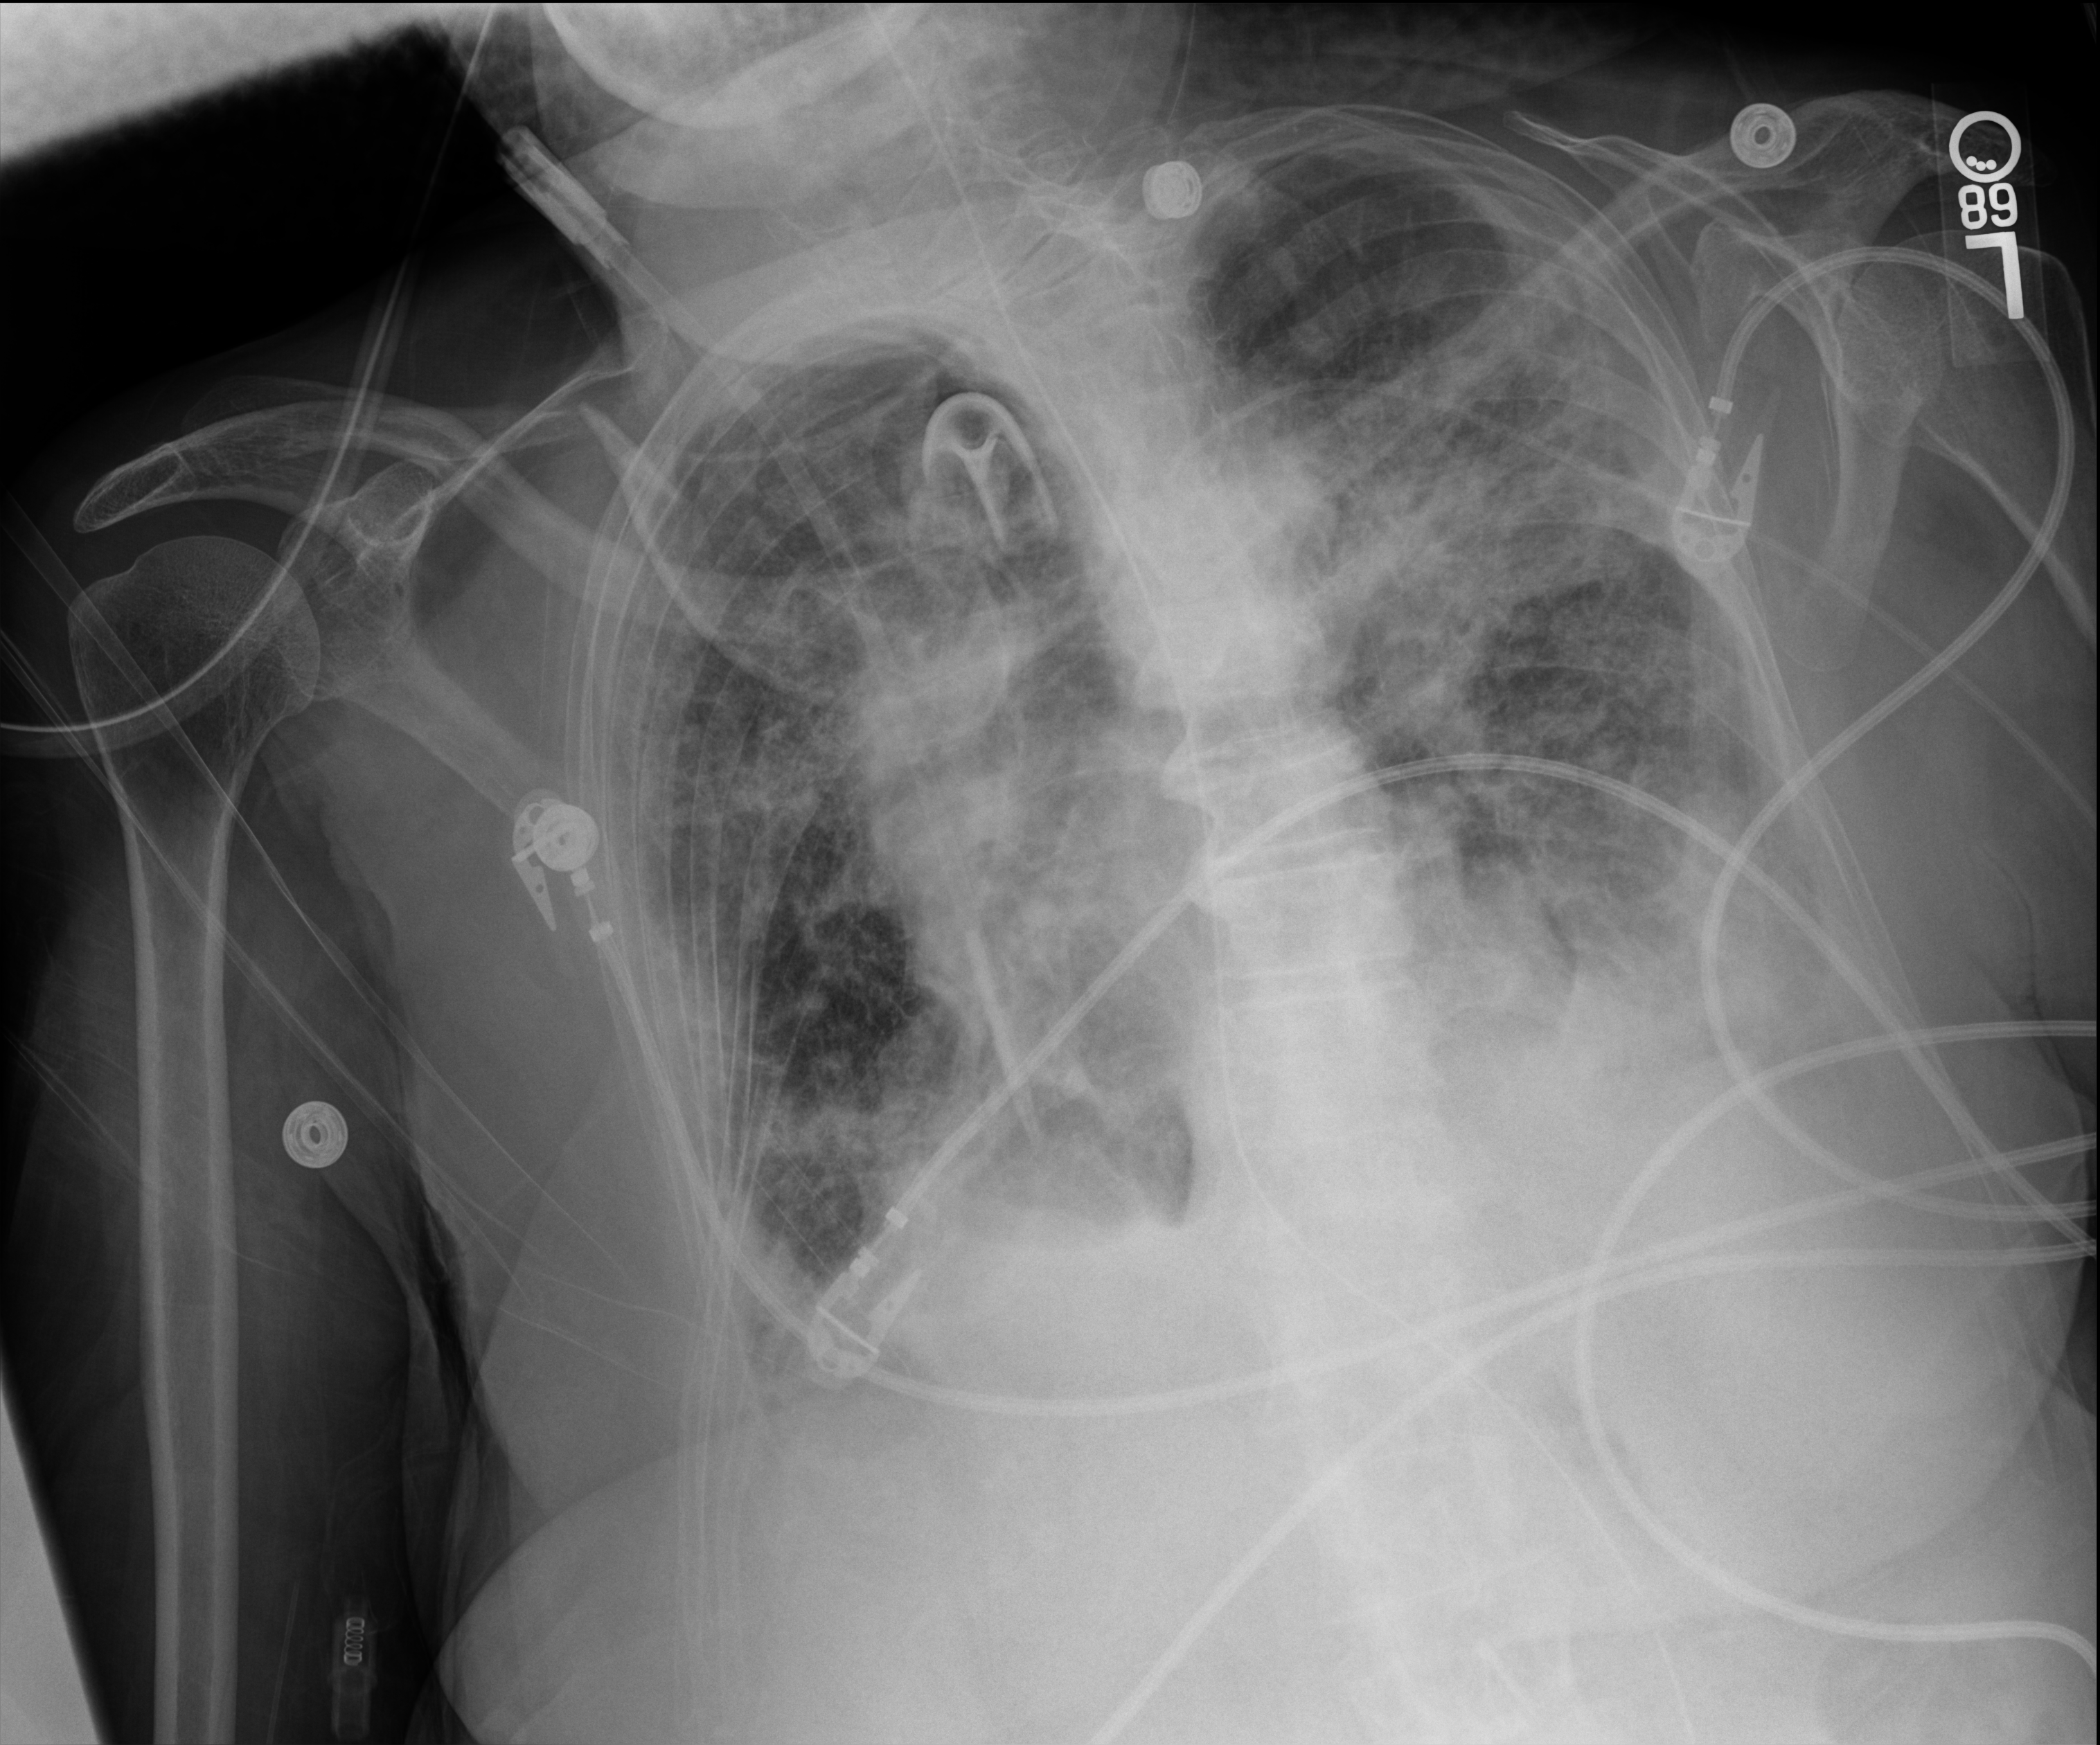
Bedside chest radiograph (digital radiography); anteroposterior (AP) projection. Female patient hospitalised with COVID-19, age 75–90 years.
From the hospital-stay record, not from the radiograph (when in the stay this image was taken is not recorded): mechanically ventilated during this hospital stay: yes.